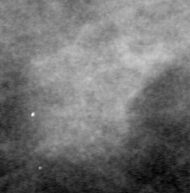
Crop from a digitized film mammogram around one marked abnormality, left breast, CC view, BI-RADS breast density category 2 (scale 1–4).
Marked abnormality: mass, shape irregular, margins ill defined; BI-RADS assessment category 4; subtlety rating 2 on a 1 (subtle) to 5 (obvious) scale; pathology (as recorded): malignant.